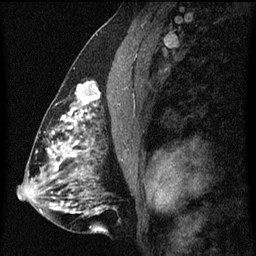
Breast MRI (dynamic contrast-enhanced), one sagittal slice. Slice 31 of 60 in the series (ordered by position). Dynamic contrast-enhanced series, image 2 of 3 at this slice position (ordered by acquisition). 1.5 T. TE 4.2 ms, TR 8 ms. 2 mm slice thickness. 256 × 256 image matrix, field of view 180 × 180 mm. Female patient, age 51 years.
Outlined on this slice (semi-automatic segmentation, software-assisted and operator-edited):
- analysis volume of interest (the breast-tissue region the enhancement analysis was run in; not a lesion): box from (x=61, y=82) to (x=102, y=129) px
- tumour enhancement mask (voxels above the 70 % enhancement threshold inside the analysis volume of interest): (x=61, y=82)–(x=100, y=129)